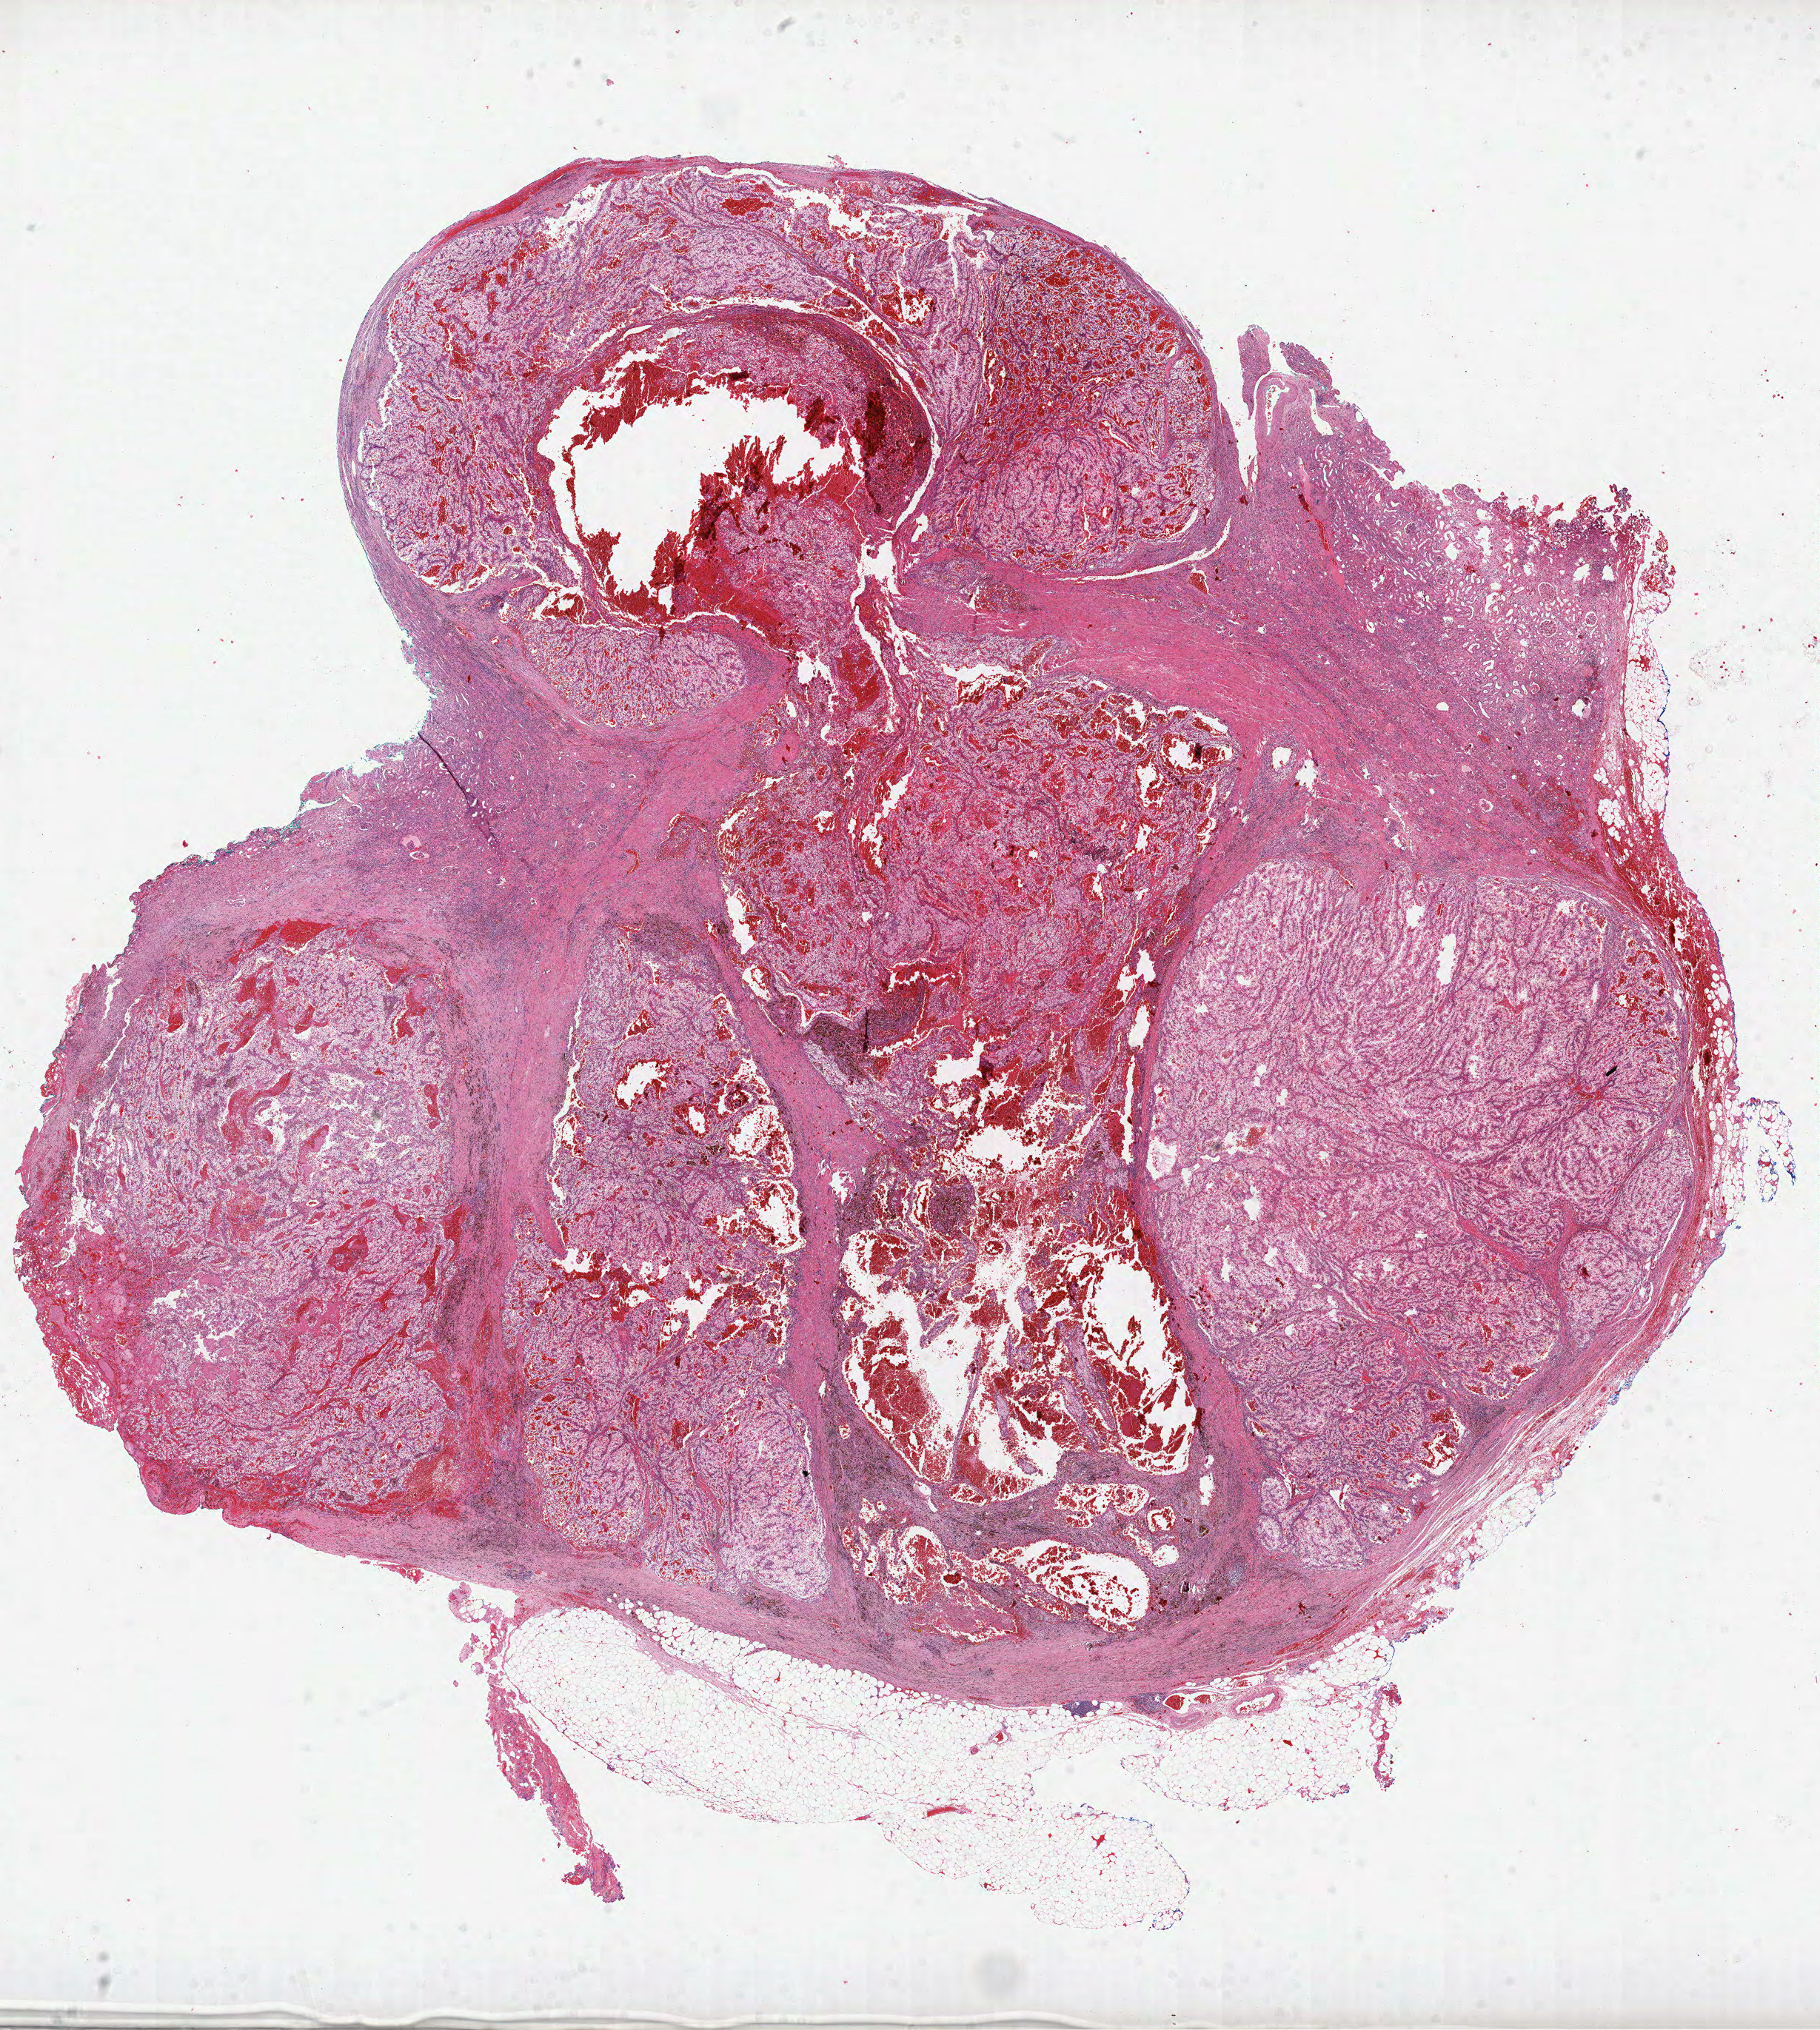
H&E whole-slide image, low-resolution overview of the scanned area, about 19.8 x 22.1 mm. Formalin-fixed paraffin-embedded (FFPE) diagnostic section. Kidney, primary tumour sample. Female, age 77 years at initial diagnosis.
Pathologic diagnosis: Clear cell adenocarcinoma, NOS.